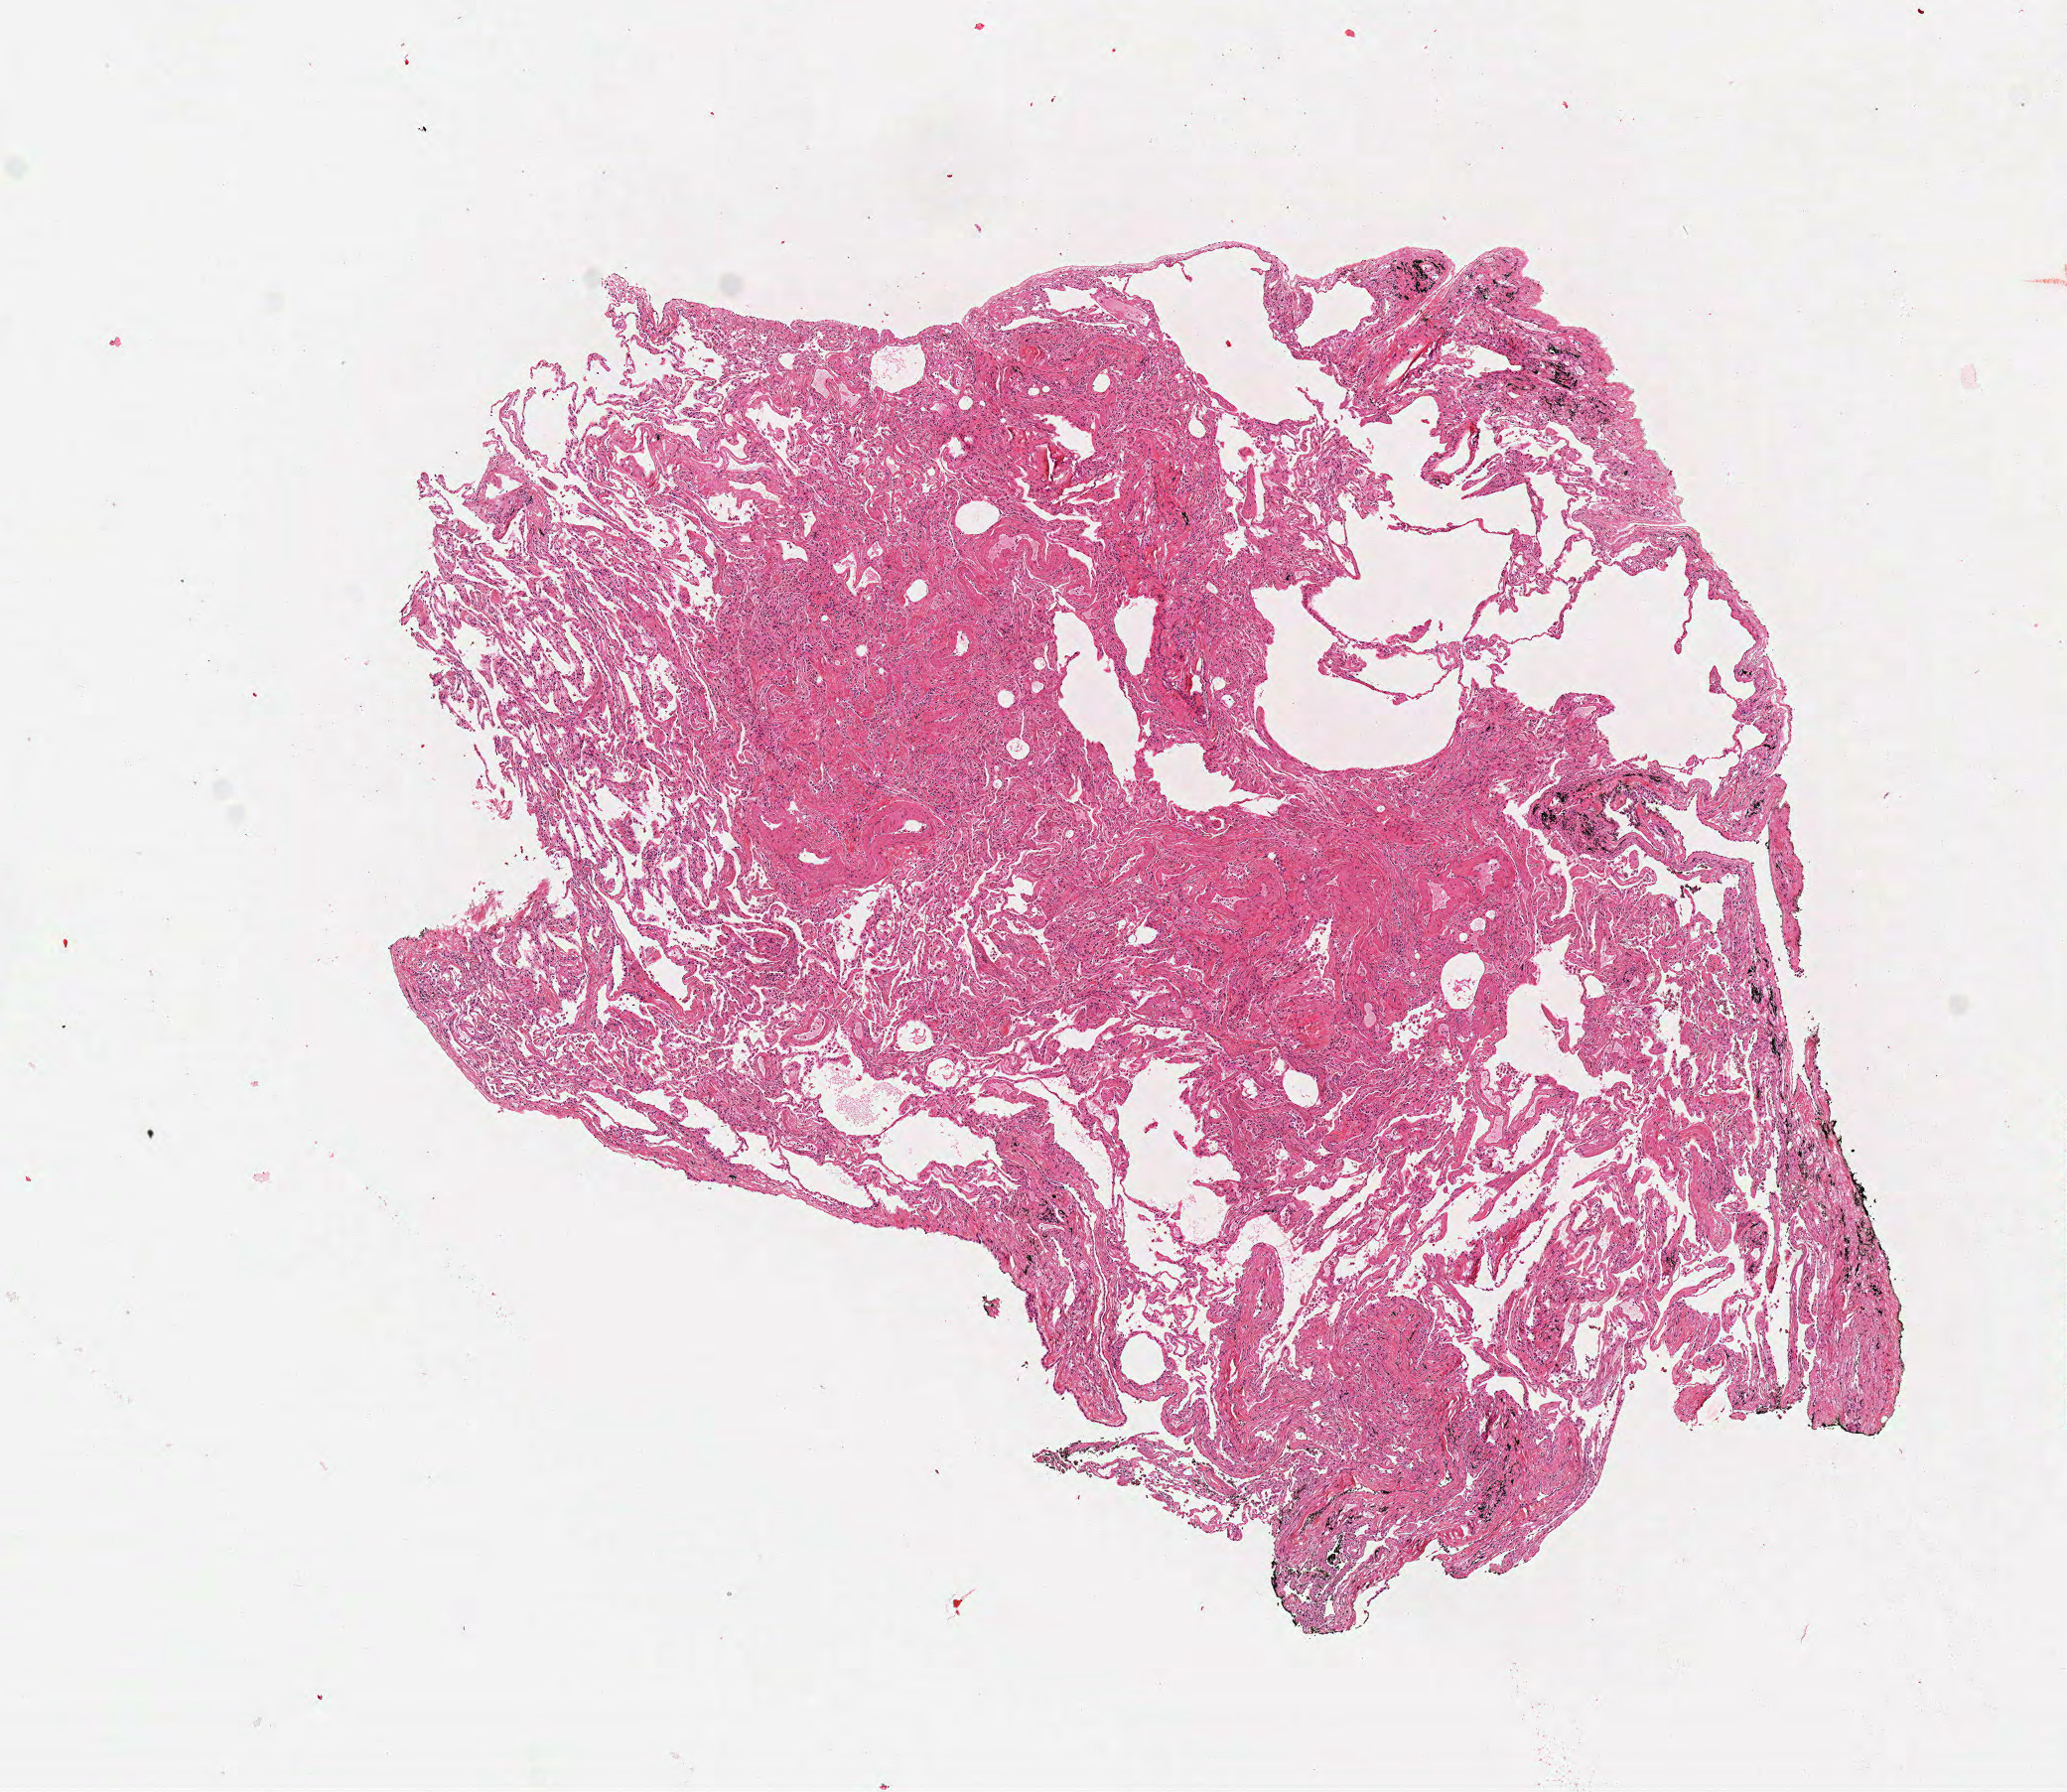
H&E-stained whole-slide image — a low-resolution overview of the entire scanned area, about 8.2 x 7.1 mm; frozen section from the top of the tissue portion; lung, solid tissue normal (non-tumour tissue) sample. Male patient; age at initial diagnosis 74 years.
- this section: solid tissue normal sample (biorepository sample class)
- patient diagnosis: Squamous cell carcinoma, NOS (upper lobe, lung)